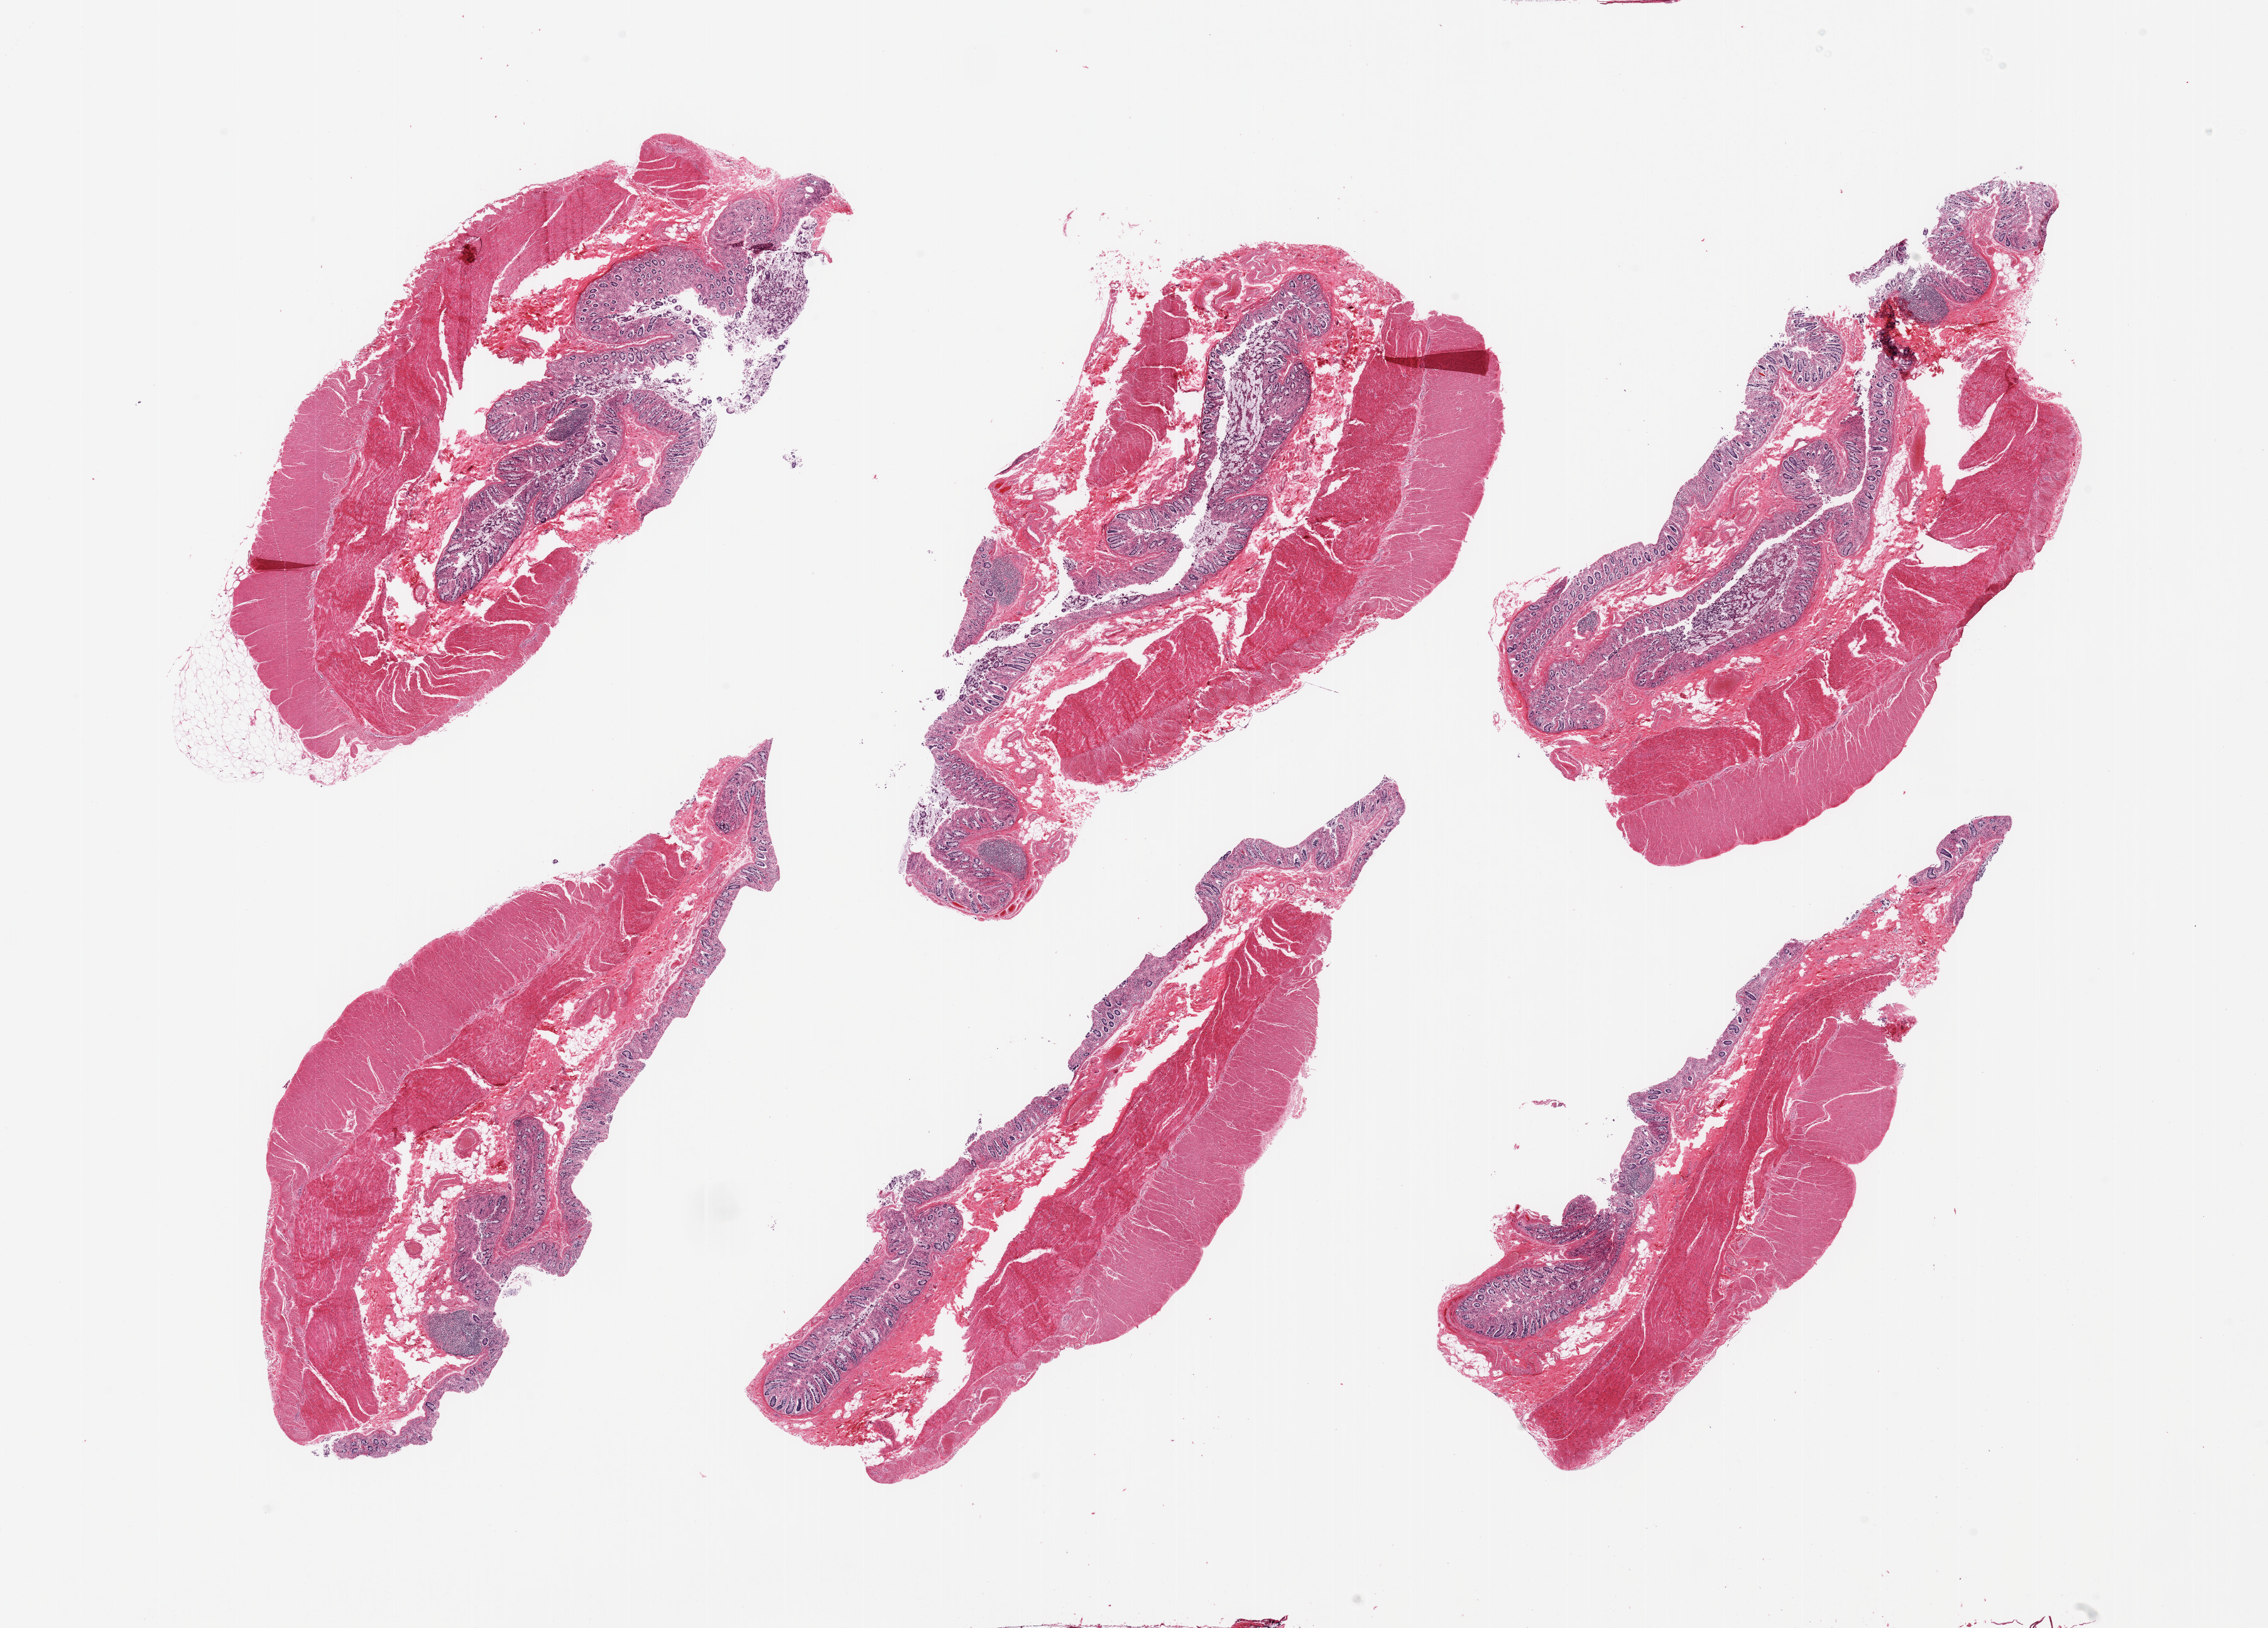
Whole-slide image, haematoxylin and eosin stain — low-resolution overview of the scanned area, about 28.5 x 20.5 mm, PAXgene-fixed, paraffin-embedded tissue, section of transverse colon (target tissue), donor tissue sample. Male donor.
• review note (as recorded): 6 pieces; some mucosal areas are severely autolyzed